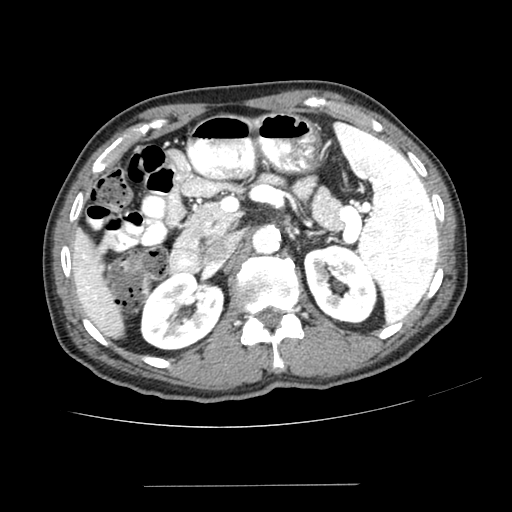
Contrast-enhanced abdominal CT (liver protocol), one axial slice. Position 139 of 187 along the scan axis. Reconstruction kernel SOFT. 100 kVp. One of 2 acquisitions stored at this slice position. Soft-tissue window (W 400 / L 40 HU). 512 × 512 image matrix, field of view 360 × 360 mm. Case-level facts recorded for this patient, not image findings: diagnosis: hepatocellular carcinoma (patient treated with transarterial chemoembolisation; whether this scan precedes or follows treatment is not stated here); TNM stage (as recorded): Stage-I; Child-Pugh class: A; tumour differentiation: poorly differentiated; tumour nodularity: uninodular.
Outlined on this slice (semi-automatically segmented with operator editing):
- liver parenchyma outside the tumour (the mass and vessels are separate outlines, so this box may not span the whole liver): bounding box <70,228,124,338> (left, top, right, bottom; pixels)
- liver vessels: <79,254,97,310>